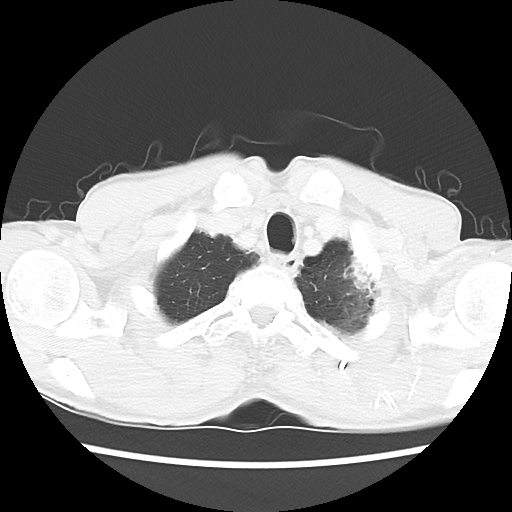
Chest CT, one axial slice. Slice 55 of 60 in the series (ordered by position). 120 kVp. Lung window (W 1500 / L -600 HU). 5 mm slice thickness. 512 × 512 image matrix, field of view 308 × 308 mm. Patient: male, 64 years. Case-level facts recorded for this patient, not image findings: clinical TNM (as recorded): T3 N3 M0; histopathological grade: G3.
Annotated regions visible in this slice (bounding box drawn by a radiologist):
- lung tumour (recorded histology: adenocarcinoma): bounding box (x1, y1, x2, y2) in pixels: (341, 248, 373, 300)